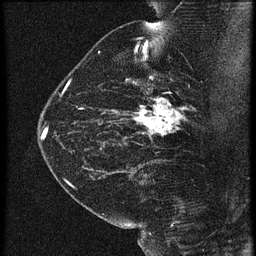
Breast MRI (dynamic contrast-enhanced), one sagittal slice; position 41 of 60 along the scan axis; 3 images stored at this slice position (order not interpretable as contrast timing); 1.5 T; TE 4.2 ms, TR 21.3 ms; 1.5 mm slice thickness; 256 × 256 image matrix, field of view 180 × 180 mm. Female patient, age 42 years. Case-level facts recorded for this patient, not image findings: setting: breast cancer imaged before/during neoadjuvant chemotherapy; receptor status: HER2-positive.
Outlined on this slice (semi-automatic segmentation, software-assisted and operator-edited):
- analysis volume of interest (the breast-tissue region the enhancement analysis was run in; not a lesion): box from (x=122, y=82) to (x=195, y=147) px
- tumour enhancement mask (voxels above the 90 % enhancement threshold inside the analysis volume of interest): (x=131, y=98)–(x=186, y=137)